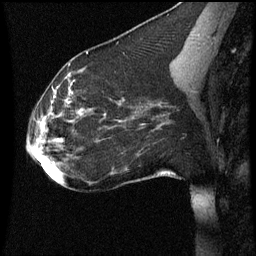
Breast MRI (dynamic contrast-enhanced), one sagittal slice. Position 27 of 60 along the scan axis. Dynamic contrast-enhanced series, image 2 of 3 at this slice position (ordered by acquisition). 1.5 T. TE 4.2 ms, TR 8.9 ms. 2 mm slice thickness. 256 × 256 image matrix. Female patient, age 35 years. Case-level facts recorded for this patient, not image findings: setting: breast cancer imaged before/during neoadjuvant chemotherapy; receptor status: HER2-positive.
Outlined on this slice (semi-automatically segmented with operator editing):
- analysis volume of interest (the breast-tissue region the enhancement analysis was run in; not a lesion): box from (x=25, y=66) to (x=177, y=177) px
- tumour enhancement mask (voxels above the 70 % enhancement threshold inside the analysis volume of interest): (x=36, y=76)–(x=91, y=155)